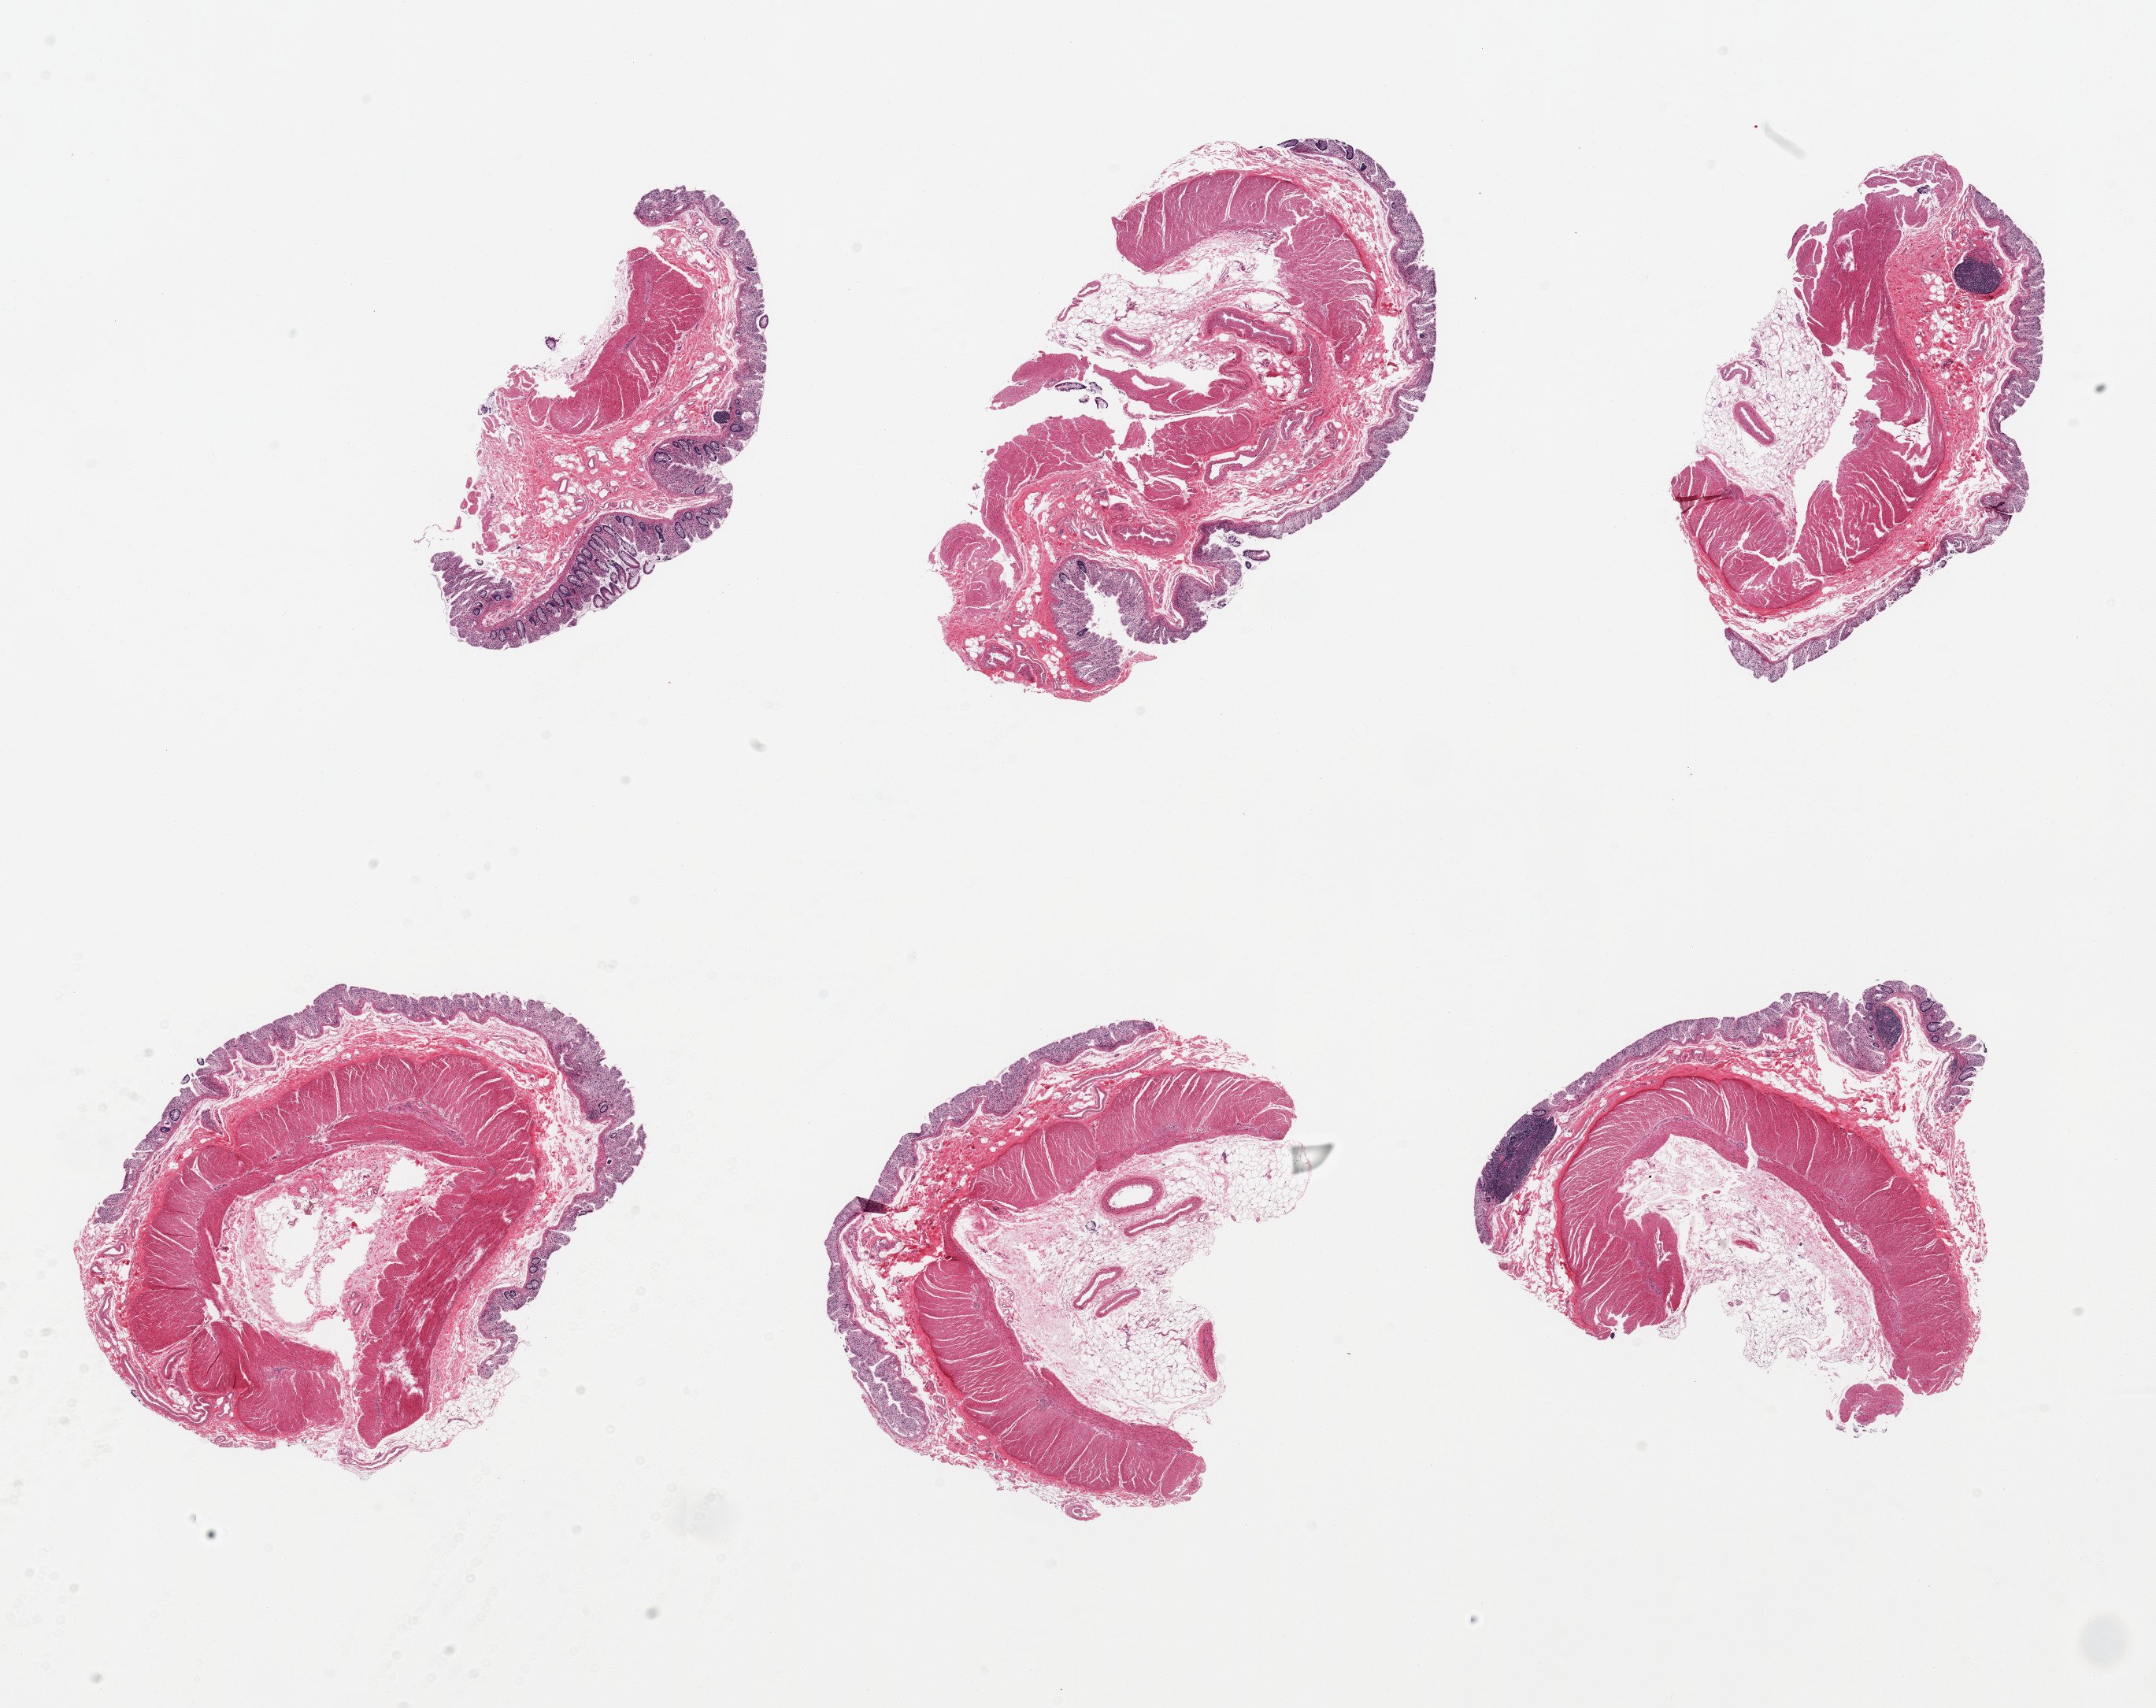
Whole-slide image, hematoxylin and eosin (H&E) stain, brightfield, a low-resolution overview of the entire scanned area, about 21.7 x 17.2 mm (slide scanned at 20x), PAXgene-fixed, paraffin-embedded tissue, sampled site (target tissue): transverse colon, tissue donor sample. Male donor.
* review note (as recorded): 6 pieces, mucosa up to ~0.5mm but glandular elements with near-total autolysis